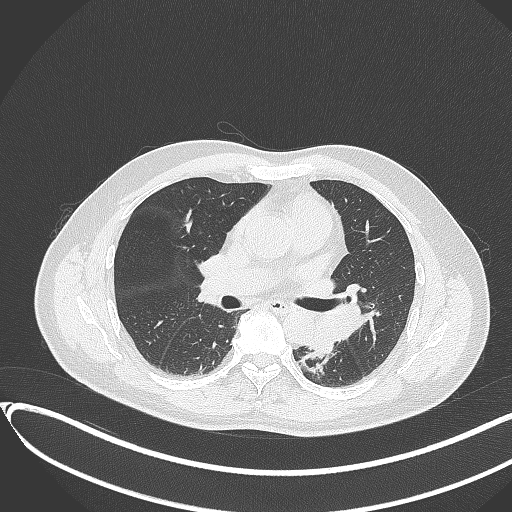
Chest CT, one axial slice; position 191 of 417 along the scan axis; 120 kVp; lung window (W 1500 / L -600 HU); 512 × 512 image matrix, field of view 400 × 400 mm. Patient: male, 54 years. From the clinical record (not read from this slice): clinical TNM (as recorded): T3 N0 M0.
Annotated regions visible in this slice (rectangle marked by the reading radiologist):
- lung tumour (recorded histology: squamous cell carcinoma): bounding box (x1, y1, x2, y2) in pixels: (308, 319, 339, 357)